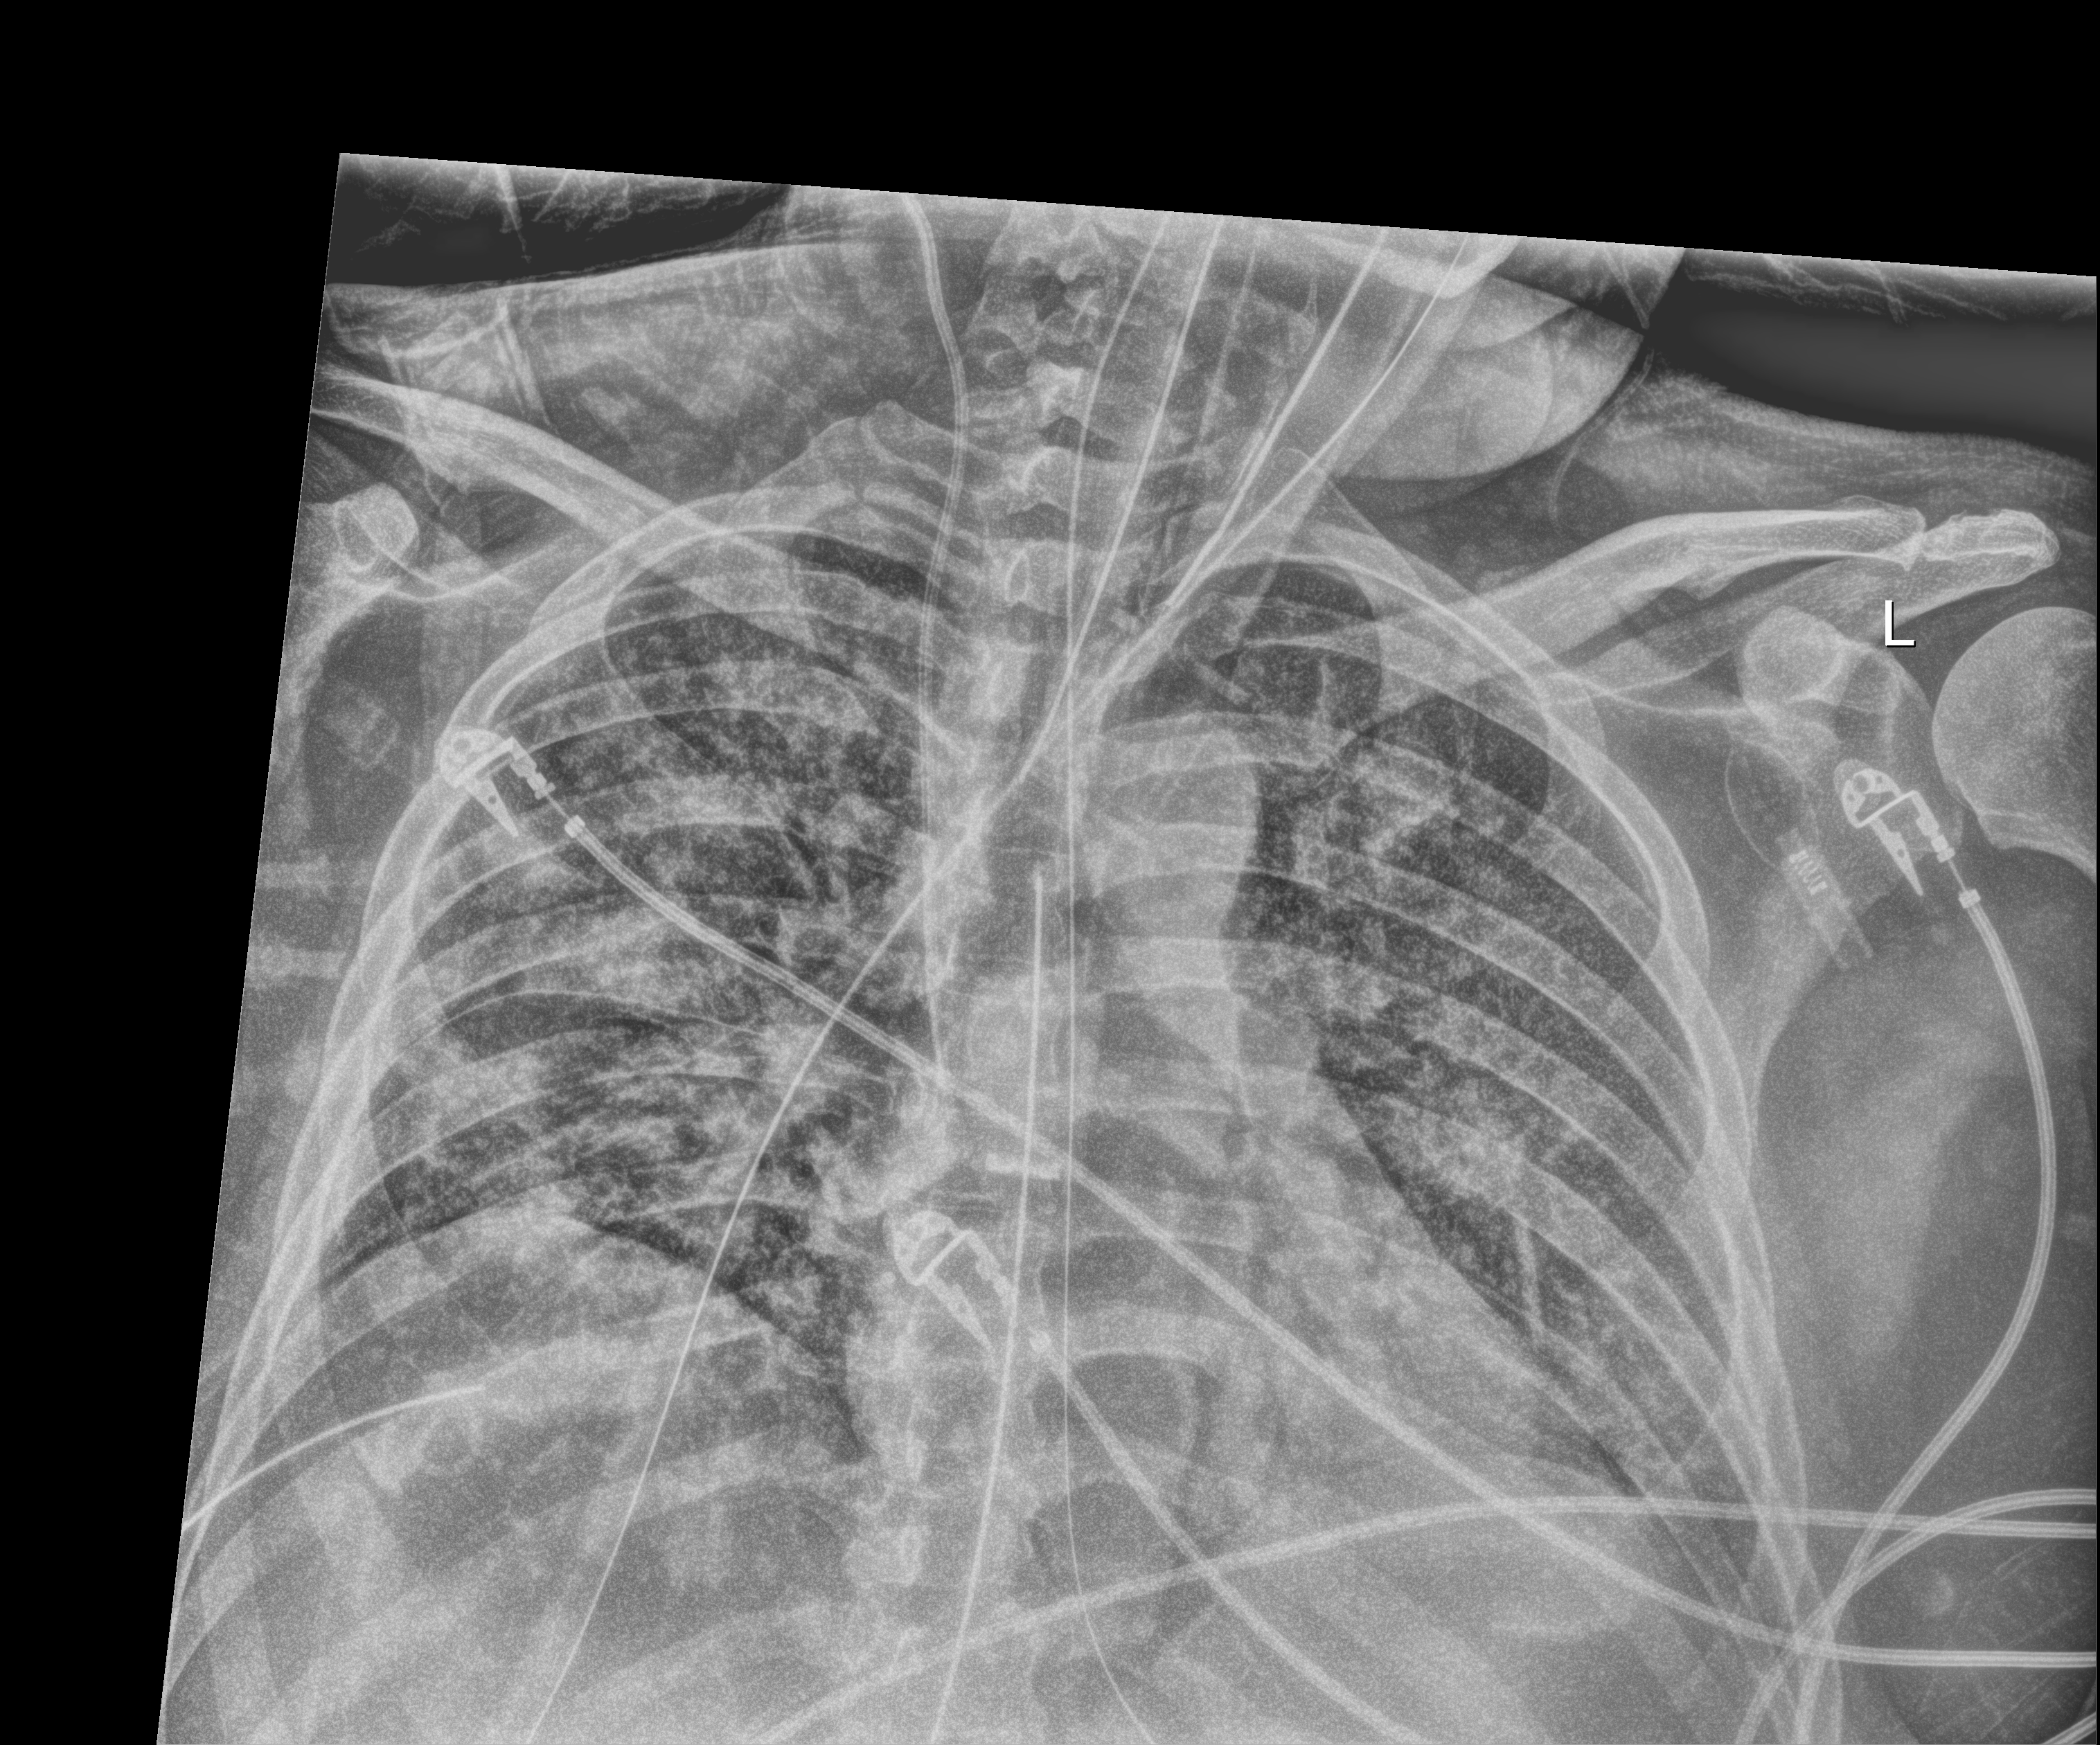
Chest X-ray (portable); anteroposterior (AP) projection. Male patient hospitalised with COVID-19, age 18–59 years.
Admission-level facts for this patient (not findings on this image; timing relative to this image not recorded): admitted to intensive care during this hospital stay: yes.